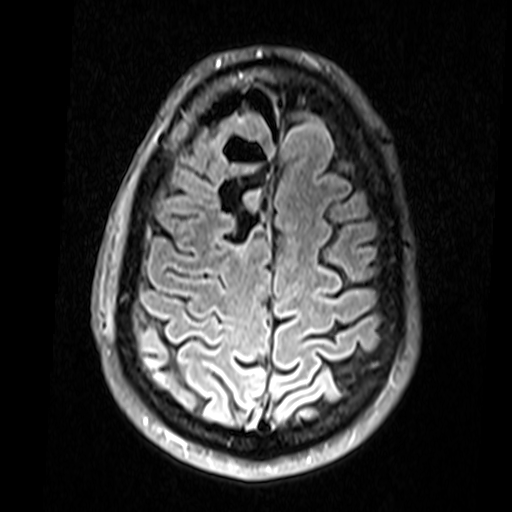
Brain MRI from a brain-tumour surgery series, one axial slice. Position 50 of 74 along the scan axis. T2 FLAIR. 3.3 mm slice thickness. 512 × 512 image matrix, field of view 220 × 220 mm. From the clinical record (not read from this slice): histopathology: Glial fibroma; tumour location: Right Frontal.
Annotated regions visible in this slice (outlined manually by an expert reader):
- residual tumour: bounding box (x1, y1, x2, y2) in pixels: (215, 190, 261, 257)